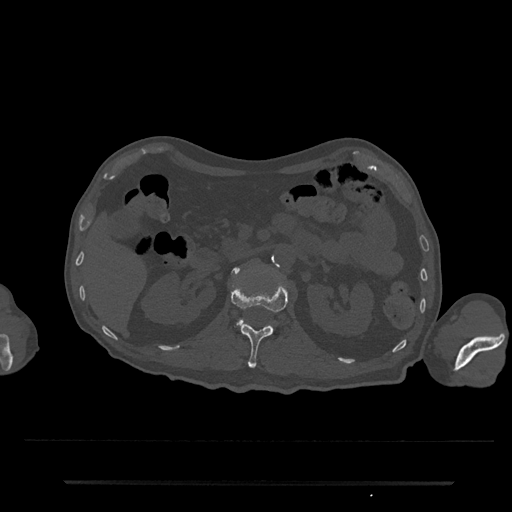
CT including the spine, one axial slice. Position 111 of 797 along the scan axis. 120 kVp. Bone window (W 1800 / L 400 HU). 0.5 mm slice thickness. 512 × 512 image matrix, field of view 427 × 427 mm. Patient: male, 74 years. From the clinical record (not read from this slice): primary cancer: prostate.
Outlined on this slice (semi-automatically segmented with operator editing):
- L1 vertebra: box from (x=231, y=283) to (x=288, y=369) px
- L2 vertebra: (x=239, y=320)–(x=243, y=326)